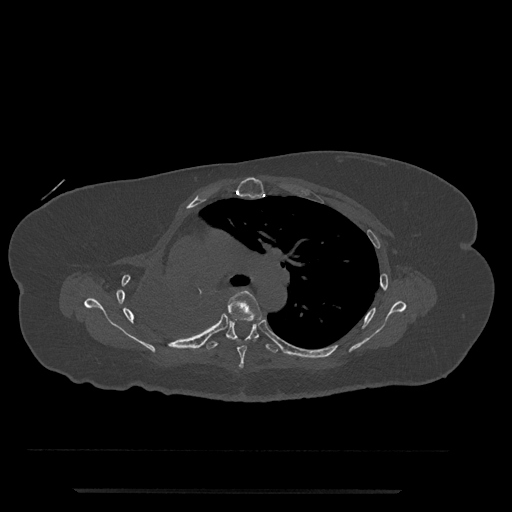
CT including the spine, one axial slice; slice 519 of 797 in the series (ordered by position); reconstruction kernel Br40s/3; 120 kVp; bone window (W 1800 / L 400 HU); 512 × 512 image matrix, field of view 440 × 440 mm. Female patient, age 51 years. Case-level facts recorded for this patient, not image findings: primary cancer: neuro; vertebrae with lytic lesions (as recorded): T8.
Structures marked on this image (semi-automatic segmentation, software-assisted and operator-edited):
- T5 vertebra: bounding box (x1, y1, x2, y2) in pixels: (197, 290, 263, 369)
- T6 vertebra: (206, 320, 278, 353)